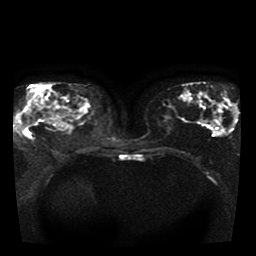
Breast MRI, one axial slice; position 18 of 41 along the scan axis; diffusion-weighted series; image 2 of 4 stored at this slice position (different b-values; order by instance number); 1.5 T; 5 mm slice thickness; 256 × 256 image matrix, field of view 330 × 330 mm. Female patient.
Annotated regions visible in this slice (expert manual segmentation):
- tumour on diffusion-weighted imaging: bounding box <18,116,36,132> (left, top, right, bottom; pixels)